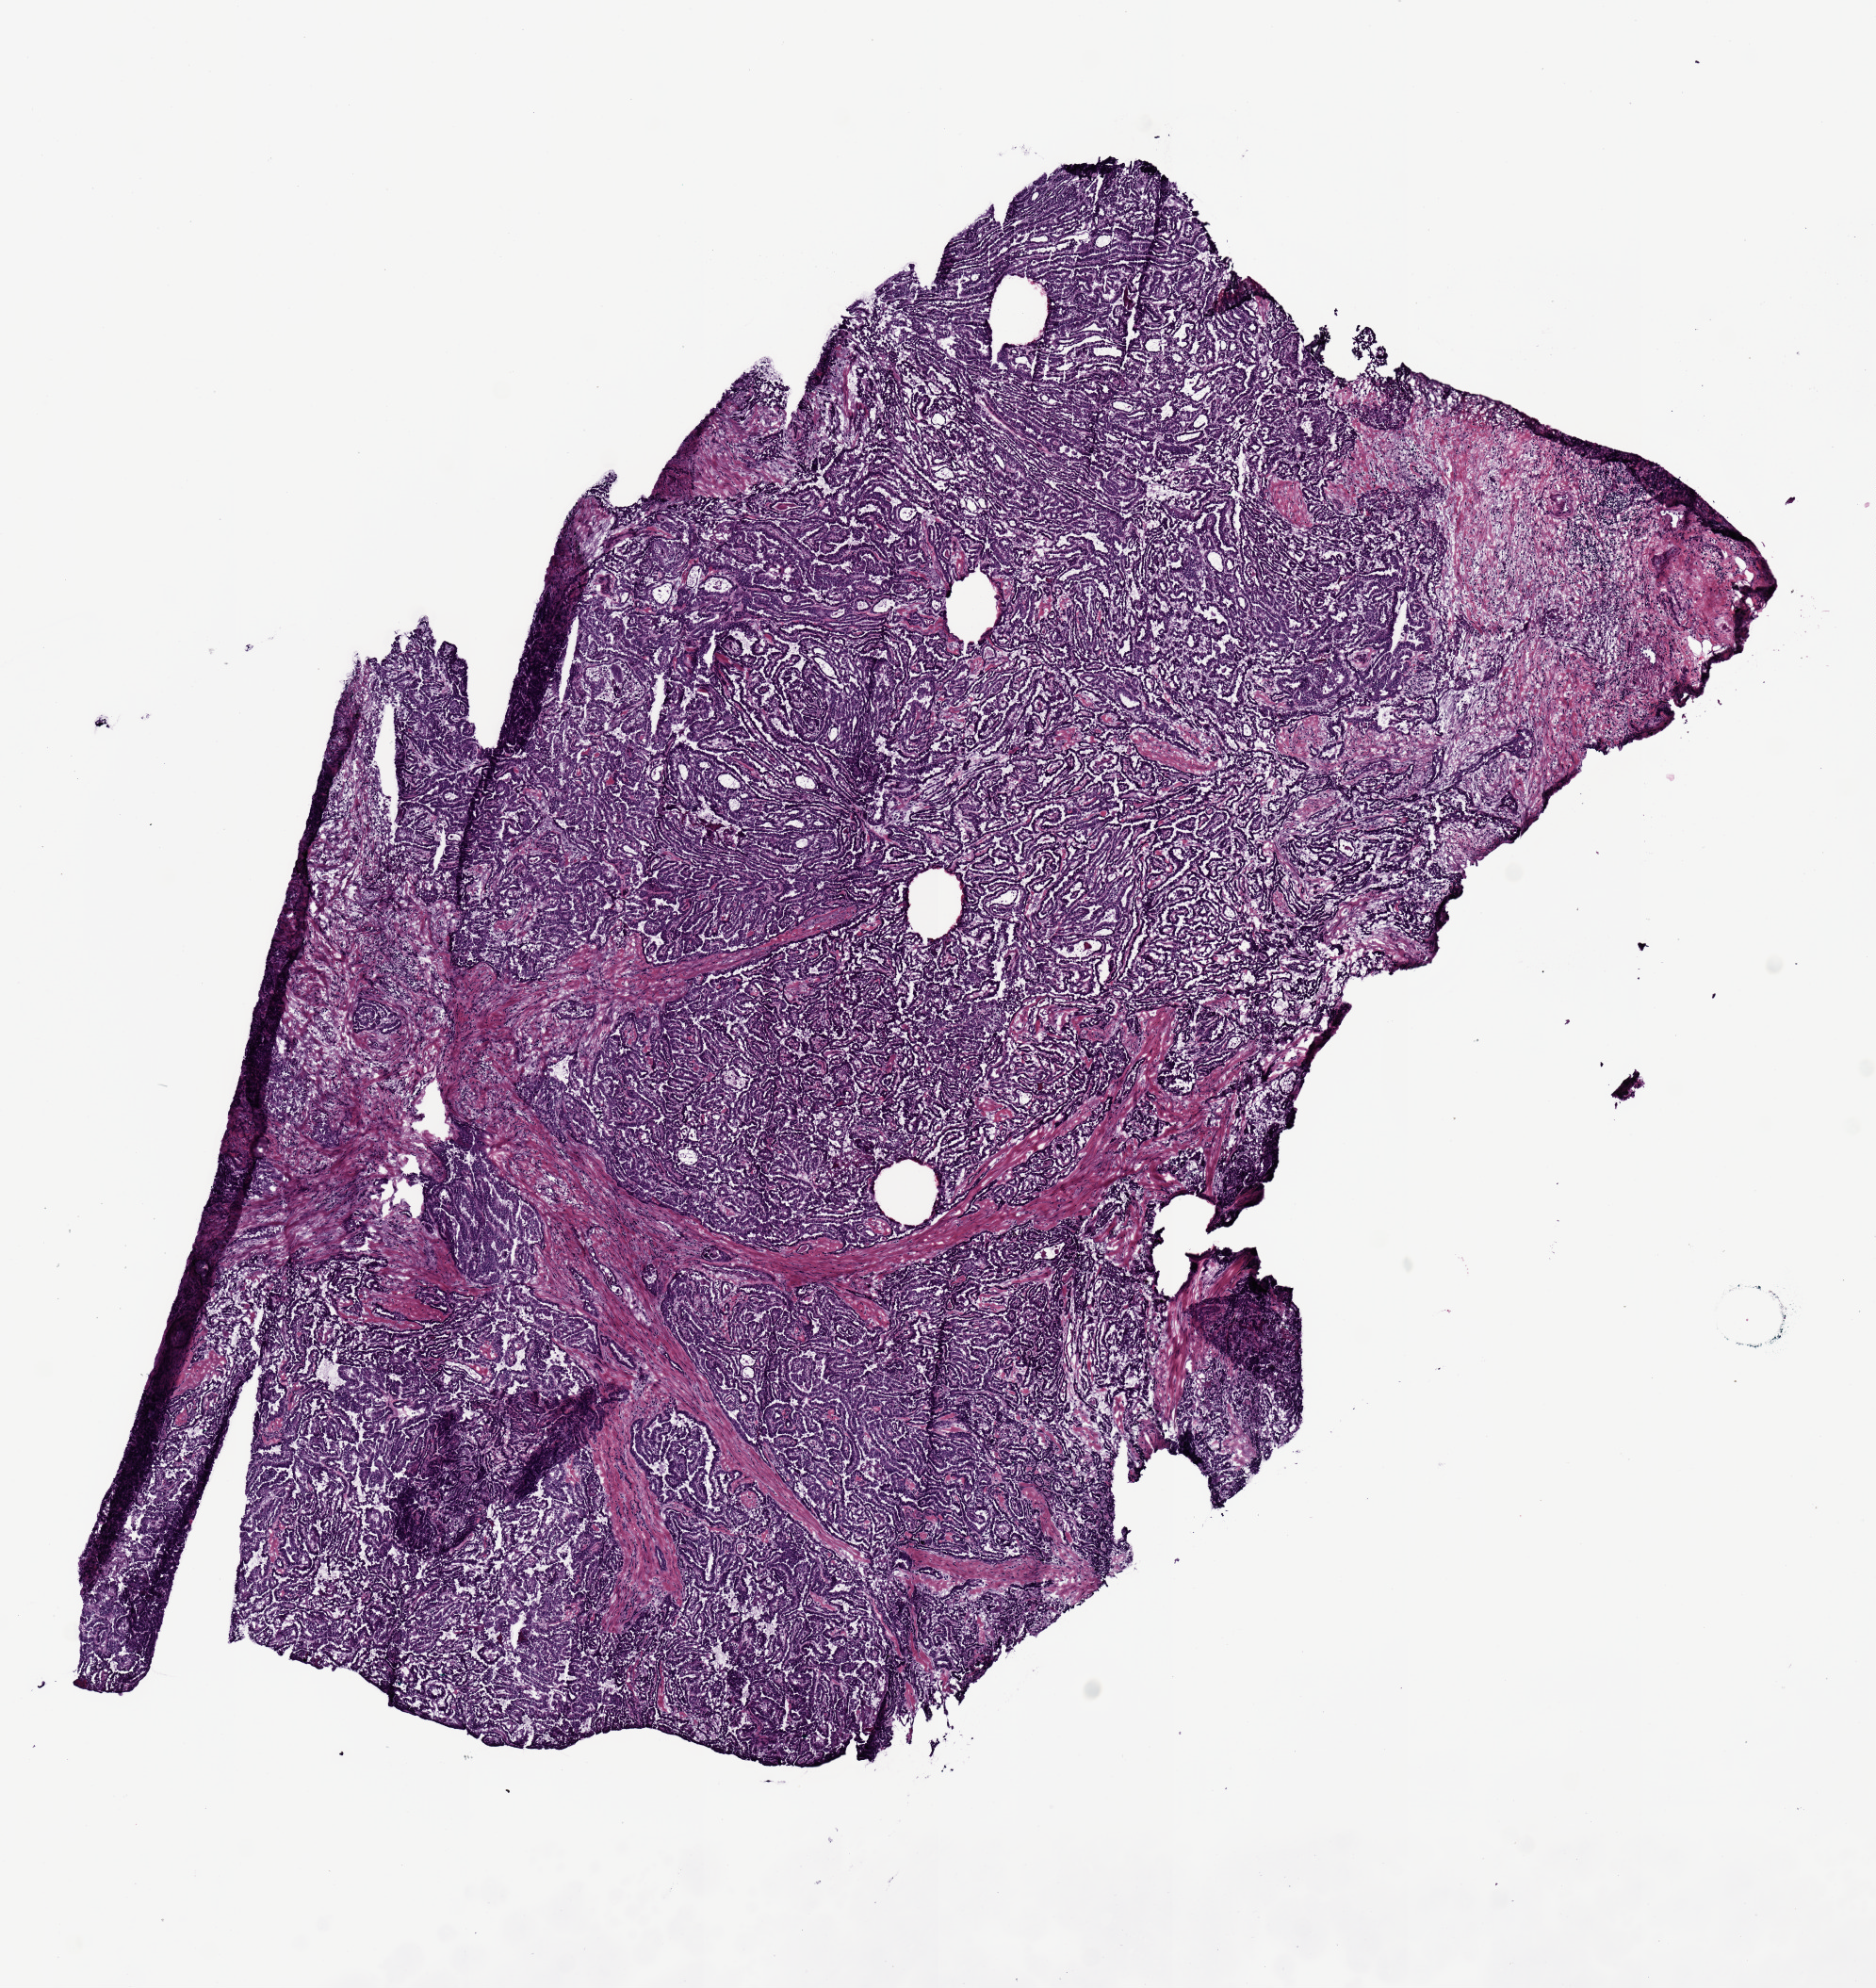
H&E-stained whole-slide image — shown as a low-resolution overview of the whole scanned area (about 7.9 x 8.3 mm, from a 20x scan), formalin-fixed paraffin-embedded (FFPE) diagnostic section, primary tumour sample from the thyroid. Female patient; age at initial diagnosis 55 years.
* TNM: T4a N1b MX
* AJCC pathologic stage: IVA (7th edition)
* histologic diagnosis: Papillary adenocarcinoma, NOS (thyroid gland)